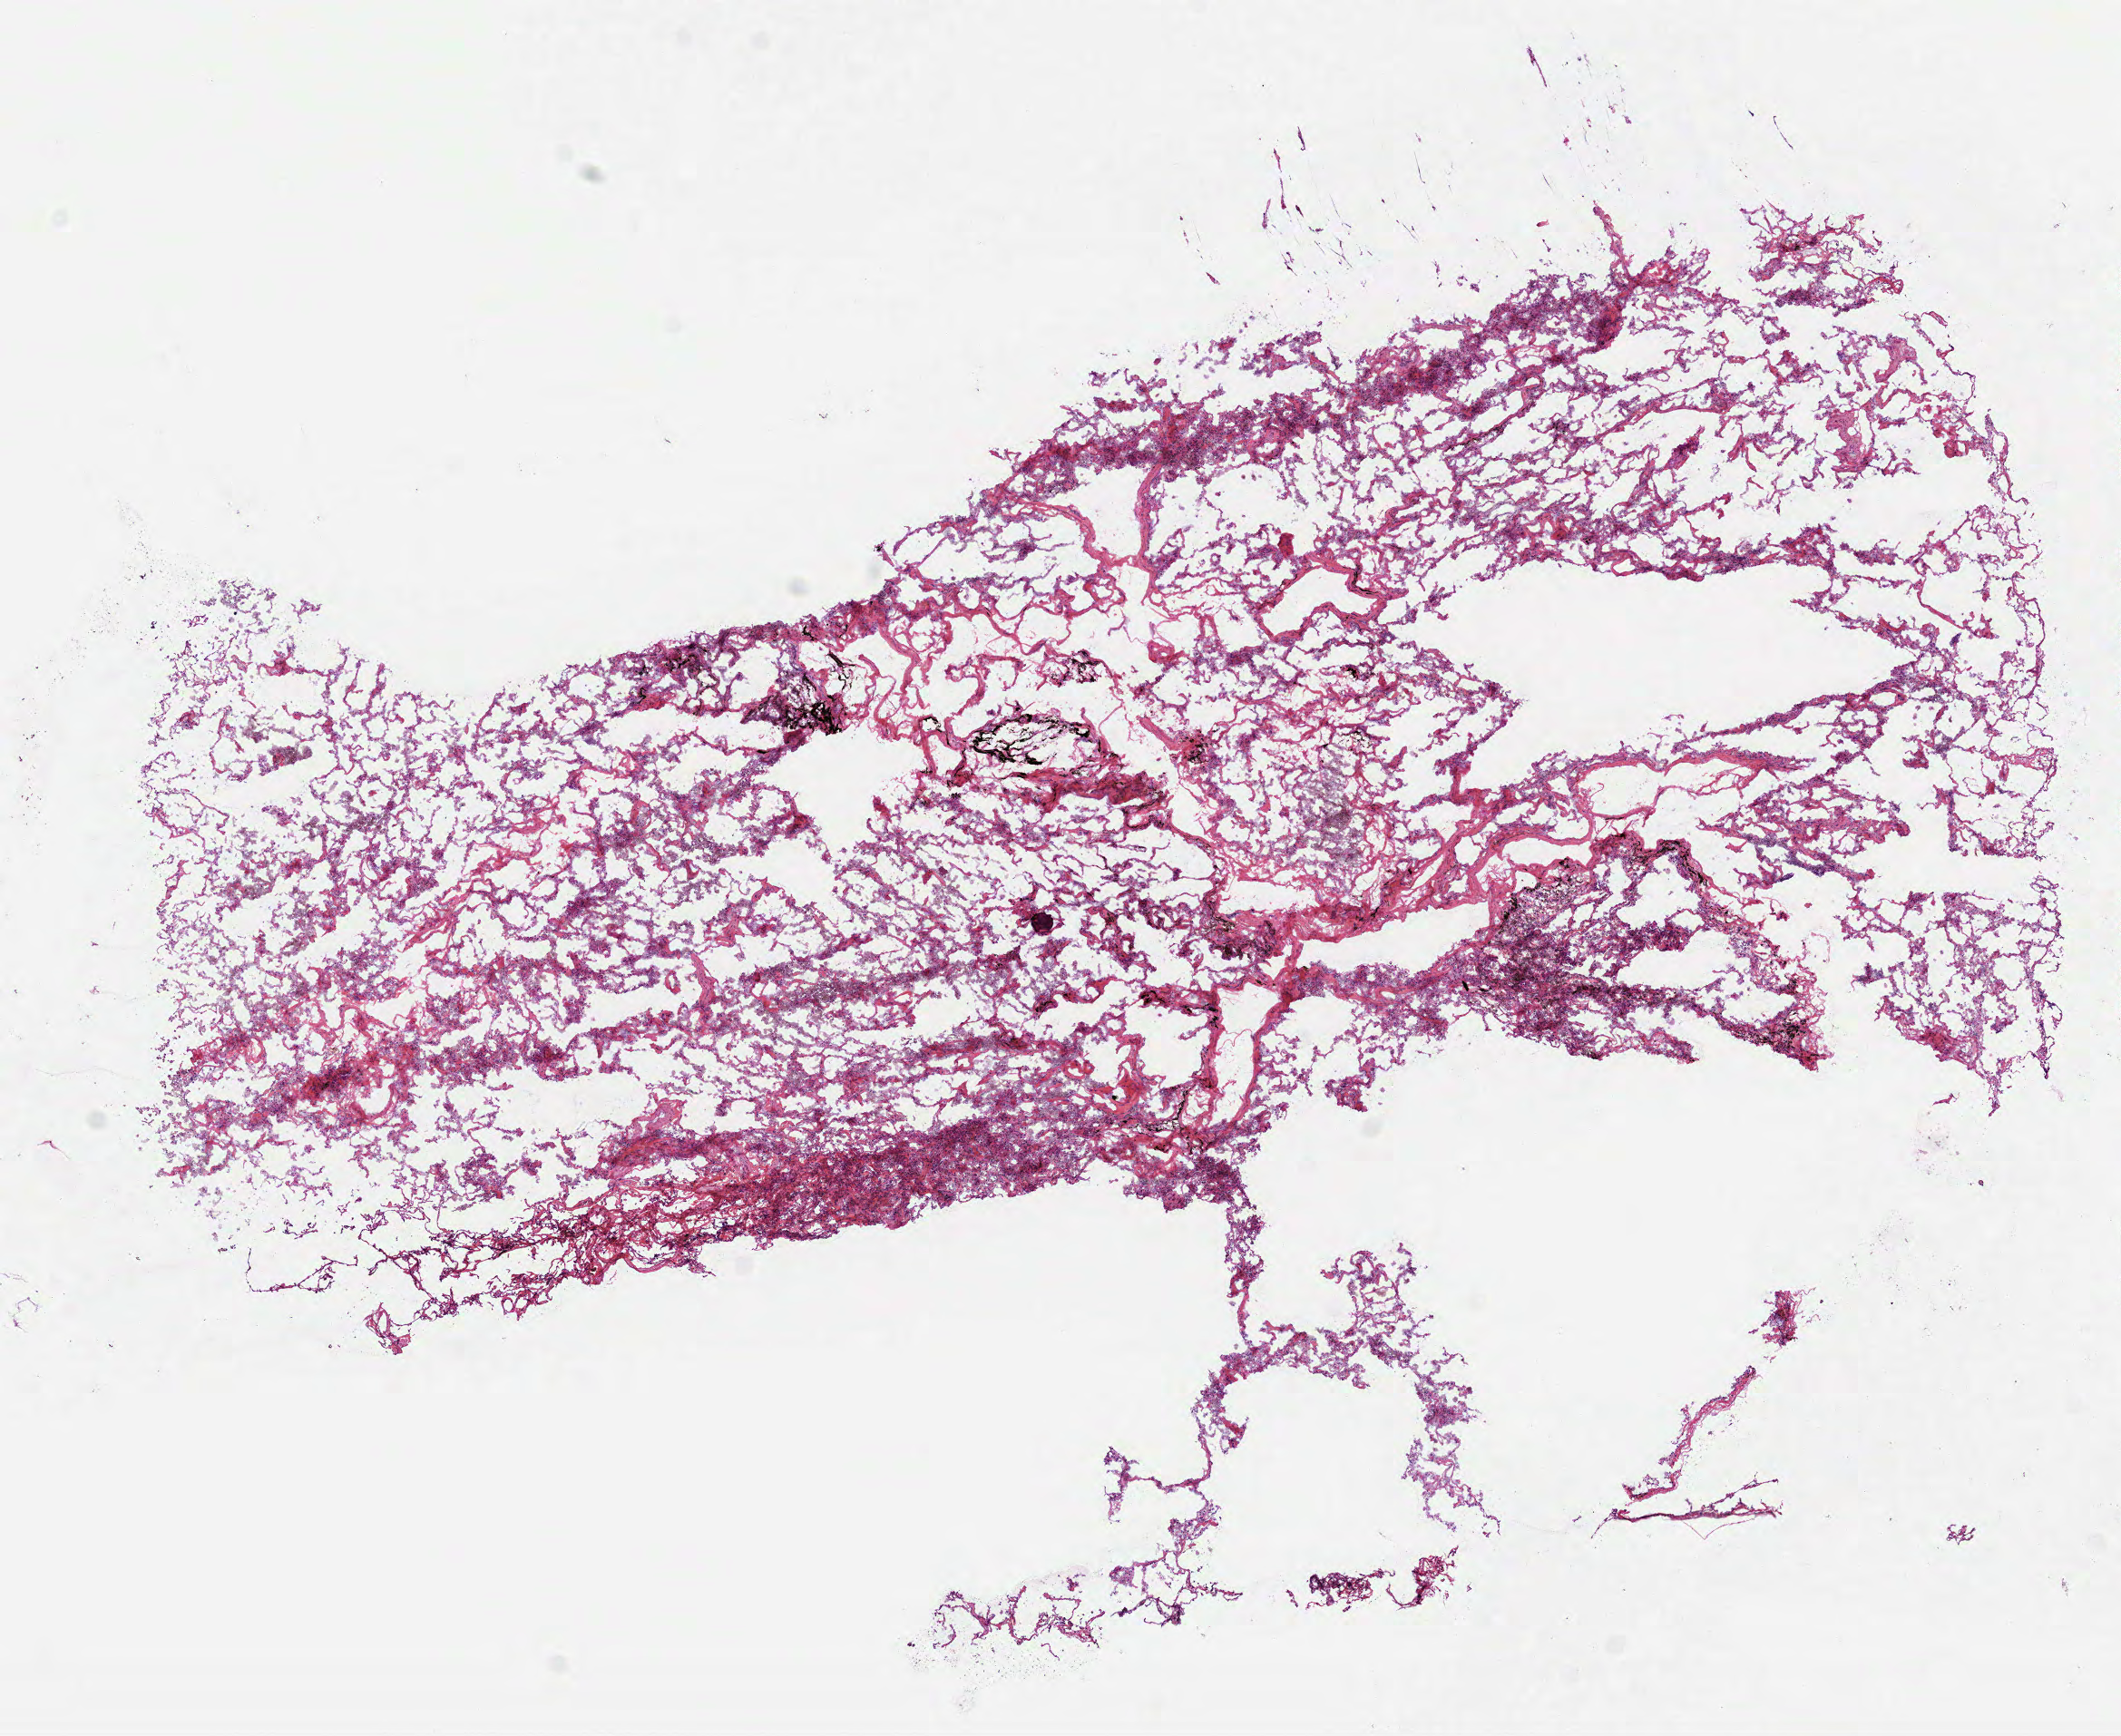
Whole-slide histology image, Hematoxylin and eosin (H&E) stained — shown as a low-resolution overview of the whole scanned area (about 9.4 x 7.7 mm, slide scanned at 40x). Frozen section from the top of the tissue portion. Sample: solid tissue normal (non-tumour tissue), lung. Patient: male, age at initial diagnosis 60 years.
• this section: solid tissue normal sample (biorepository sample class)
• patient diagnosis: Adenocarcinoma, NOS (lower lobe, lung)